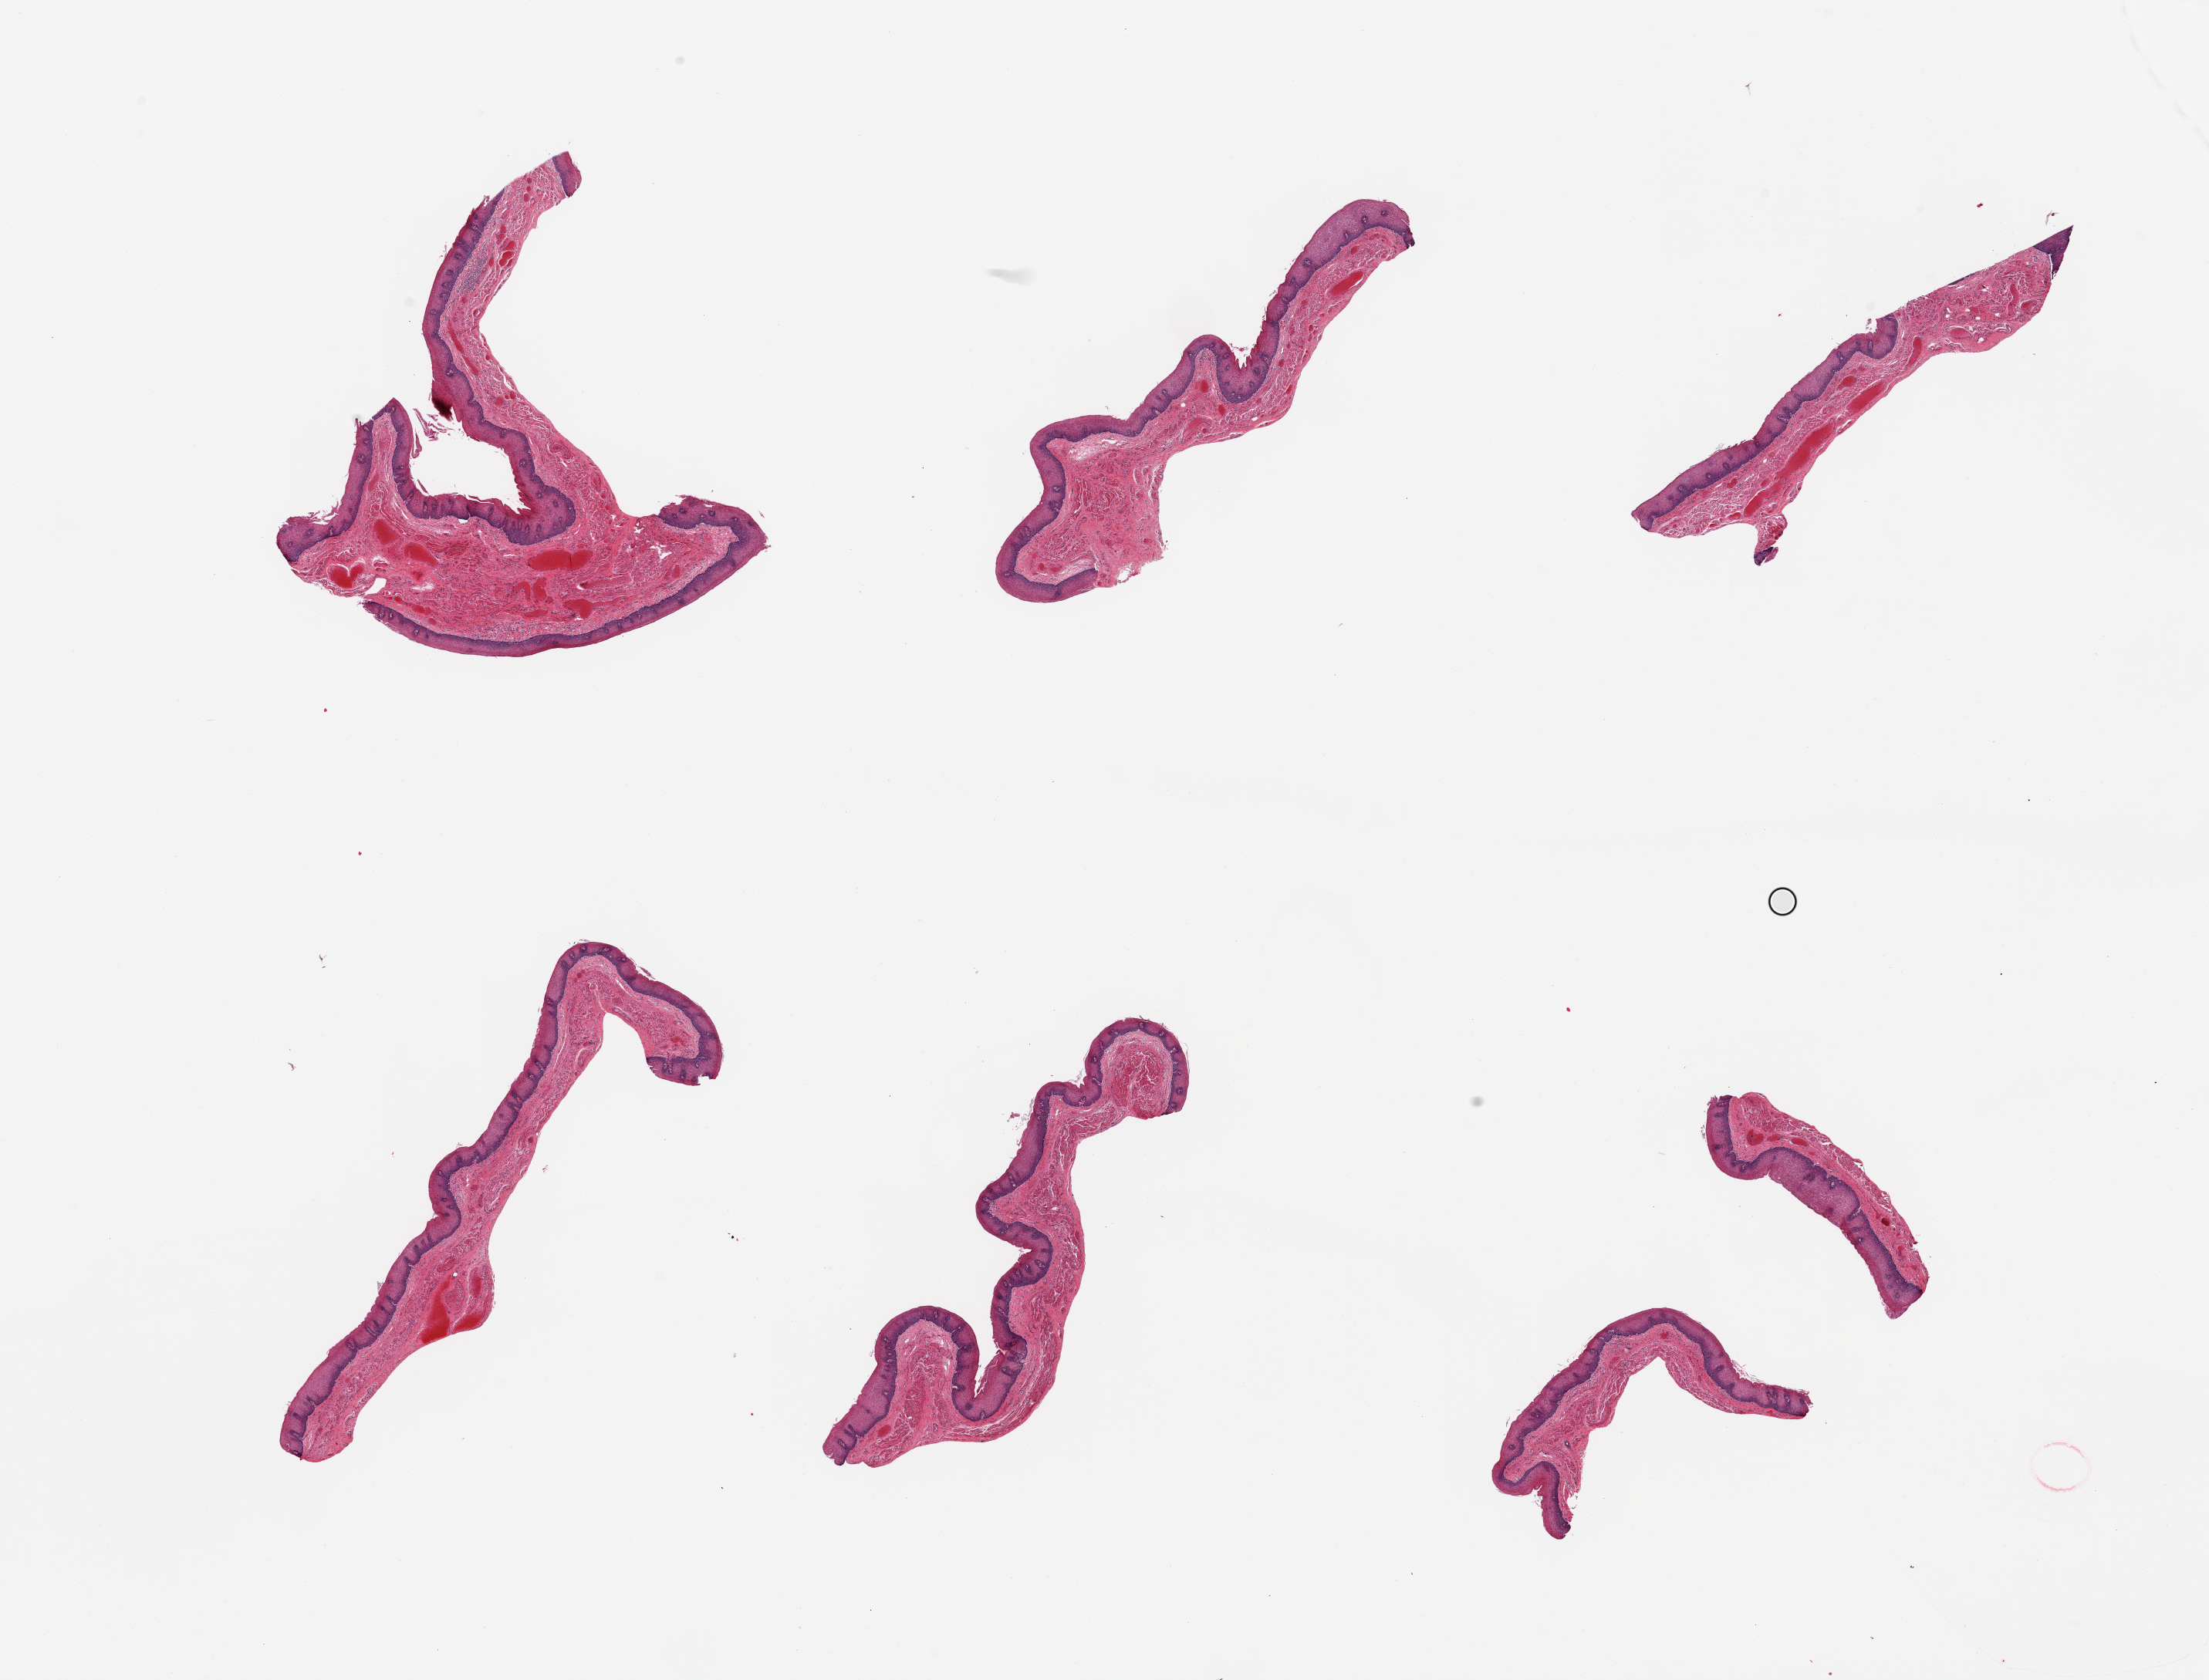
Whole-slide image, hematoxylin and eosin (H&E) stain, brightfield — shown as a low-resolution overview of the whole scanned area (about 22.6 x 17.2 mm, acquisition: 20x scan), PAXgene-fixed, paraffin-embedded tissue, sampled site (target tissue): esophageal mucous membrane, donor tissue sample. Female donor.
* reviewer comment on this tissue sample: 6 pieces; slight surface desquamation; moderate vascular congestion; well dissected